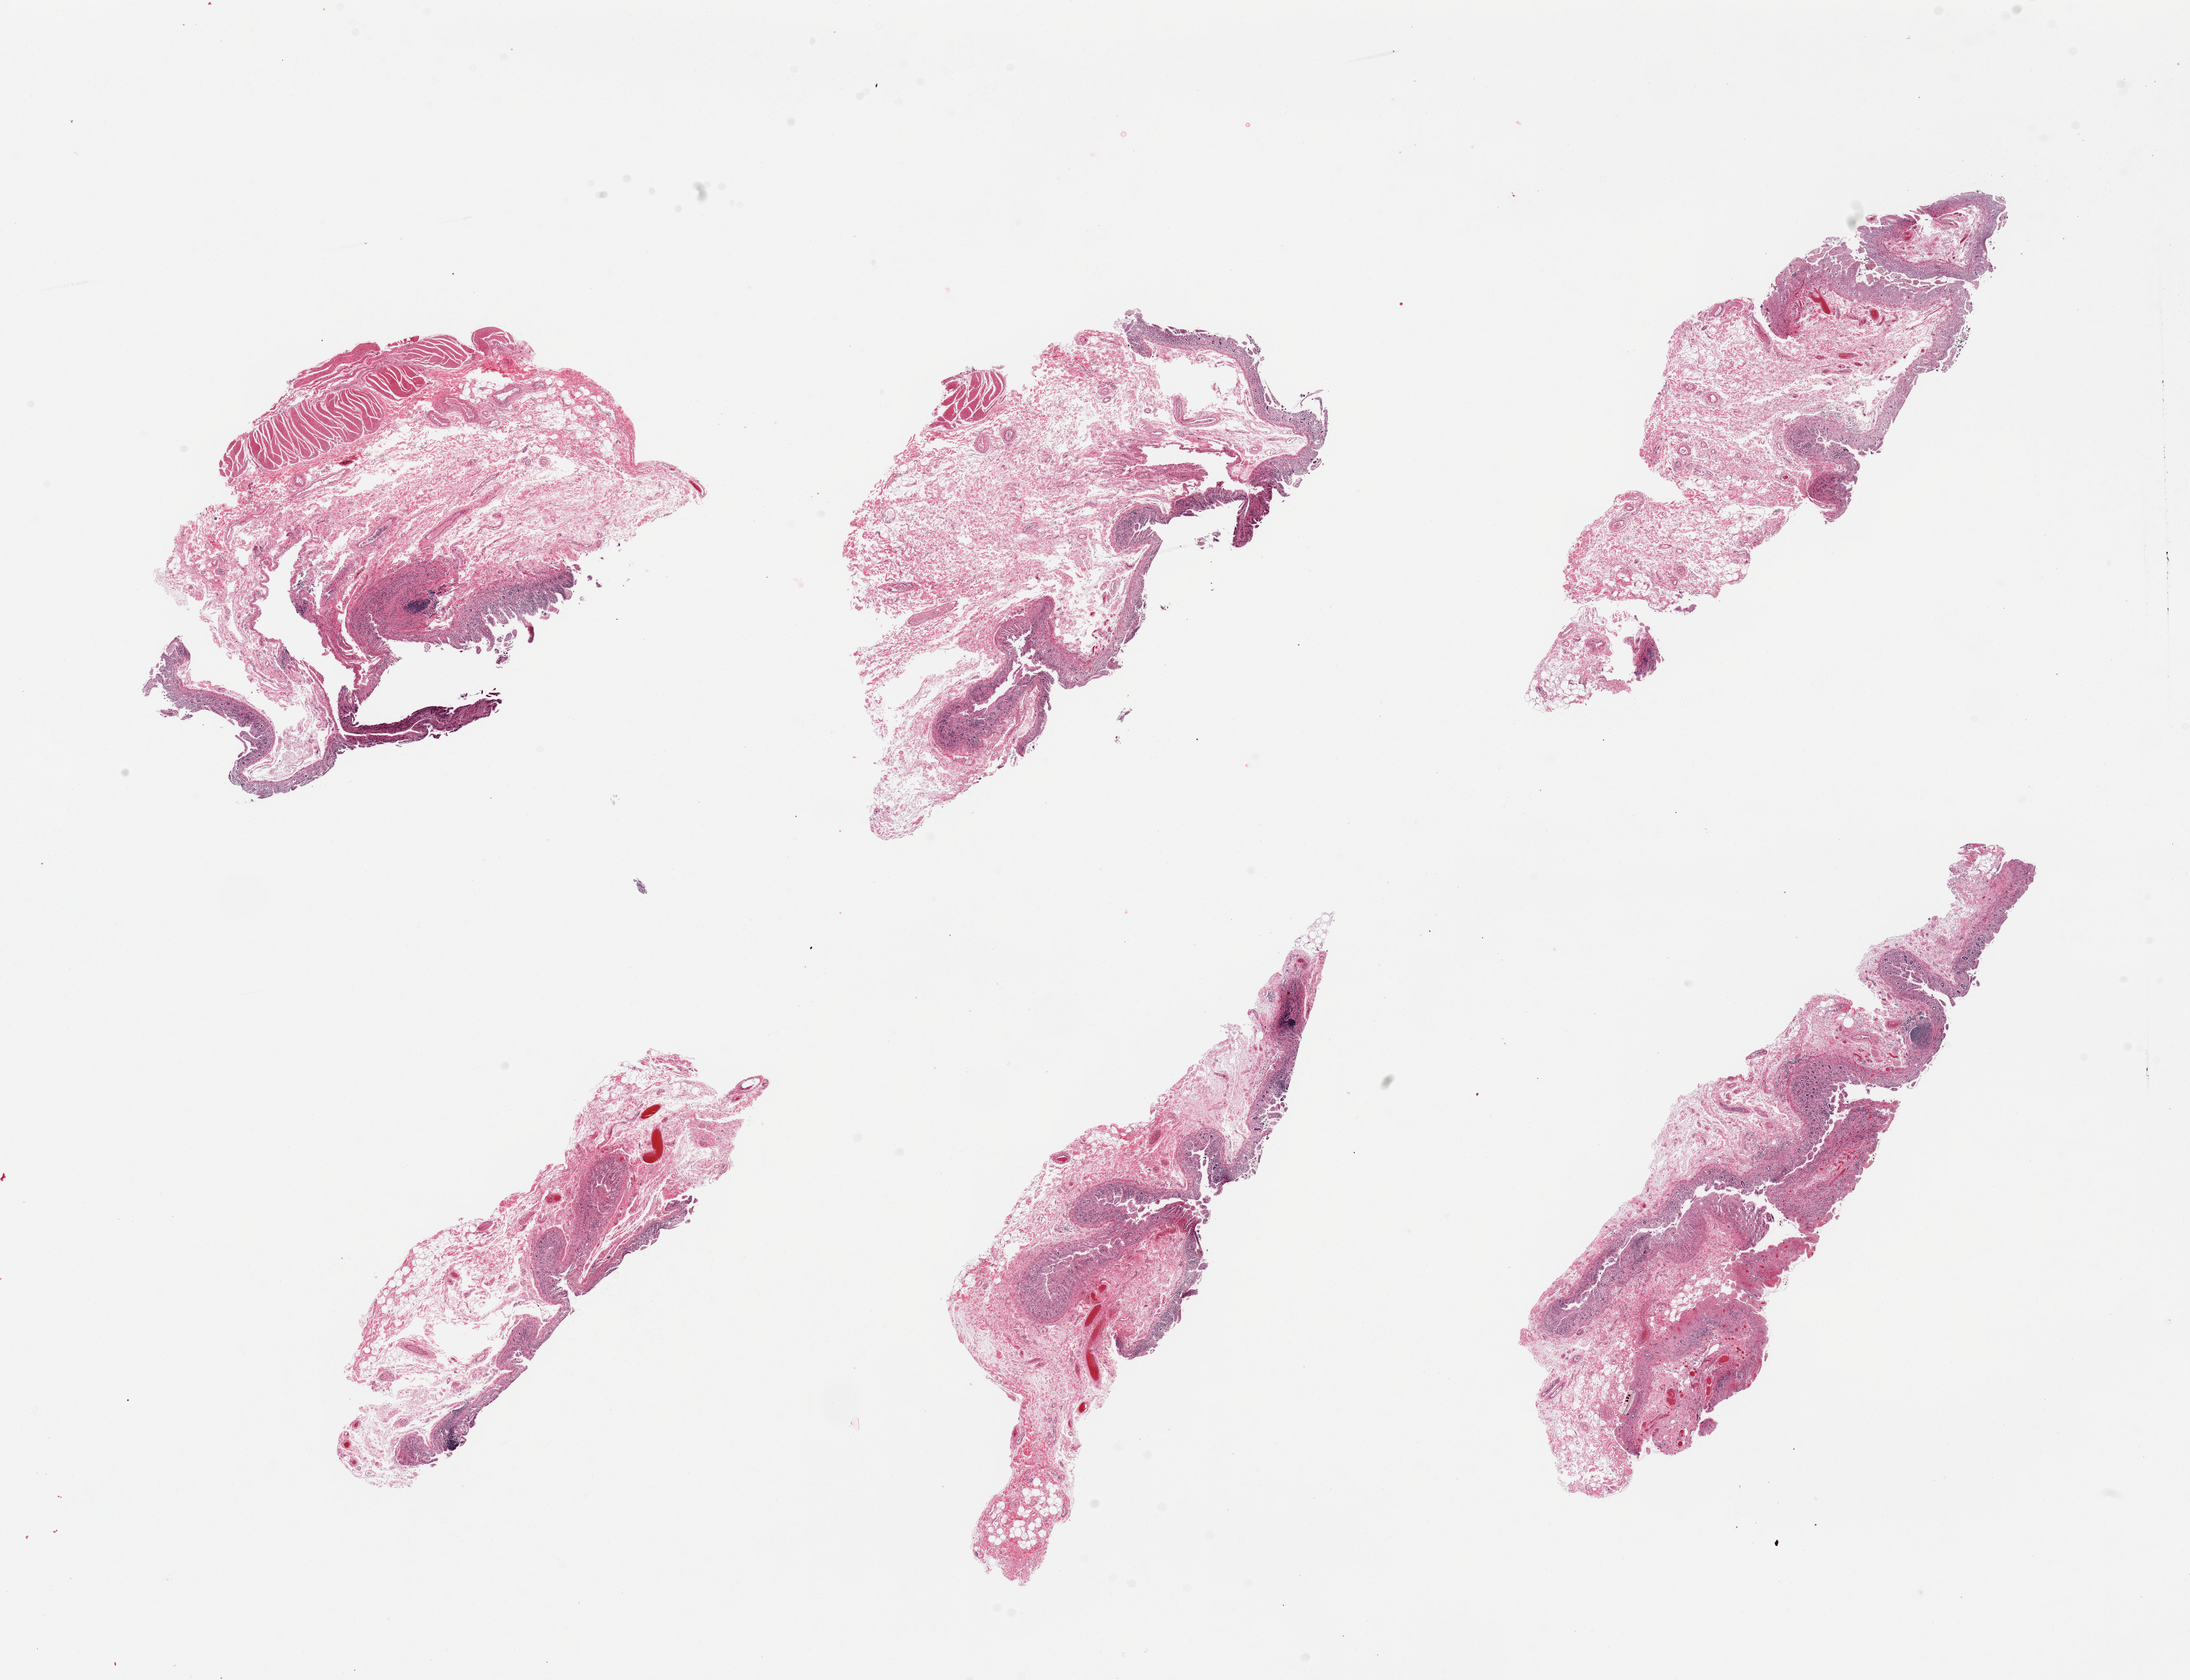
Whole-slide image, hematoxylin and eosin (H&E) stain, shown as a low-resolution overview of the whole scanned area (about 26.6 x 20.4 mm, from a 20x scan). Donor sex: male.
- specimen: PAXgene-fixed paraffin-embedded (PFPE) section; target tissue: ileum; tissue donor sample